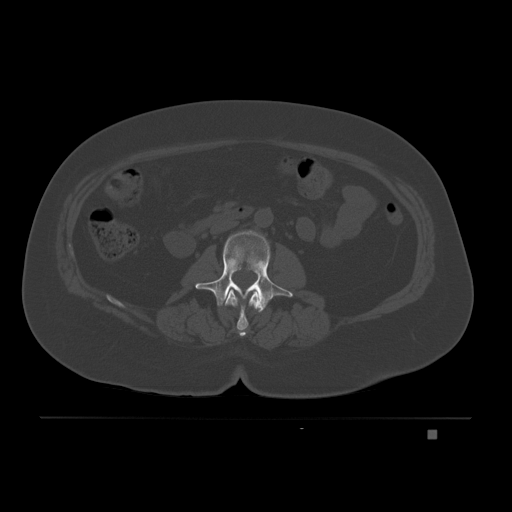
CT including the spine, one axial slice; position 62 of 221 along the scan axis; bone window (W 1800 / L 400 HU); 3 mm slice thickness; 512 × 512 image matrix, field of view 474 × 474 mm. Patient: female, 63 years. From the clinical record (not read from this slice): primary cancer: breast.
Structures marked on this image (semi-automatically segmented with operator editing):
- L1 vertebra: bounding box [x1, y1, x2, y2] px = [224, 289, 260, 336]
- L2 vertebra: [196, 230, 293, 314]